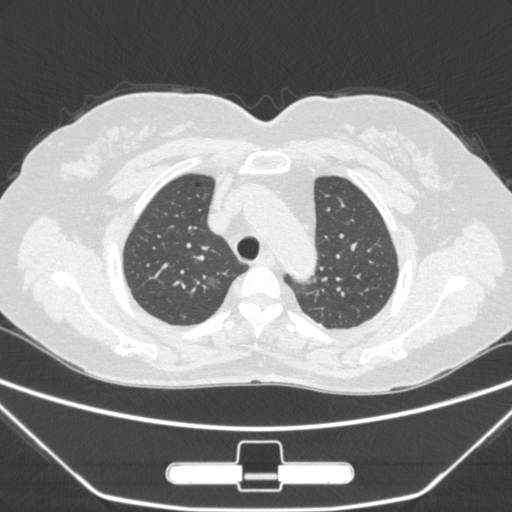
Chest CT, one axial slice; position 222 of 275 along the scan axis; 120 kVp; lung window (W 1500 / L -600 HU); 1 mm slice thickness; 512 × 512 image matrix, field of view 356 × 356 mm. Female patient, age 63 years. Case-level facts recorded for this patient, not image findings: clinical TNM (as recorded): T1a N0 M0; histopathological grade: G1.
Outlined on this slice (rectangle marked by the reading radiologist):
- lung tumour (recorded histology: adenocarcinoma): box from (x=200, y=268) to (x=233, y=300) px